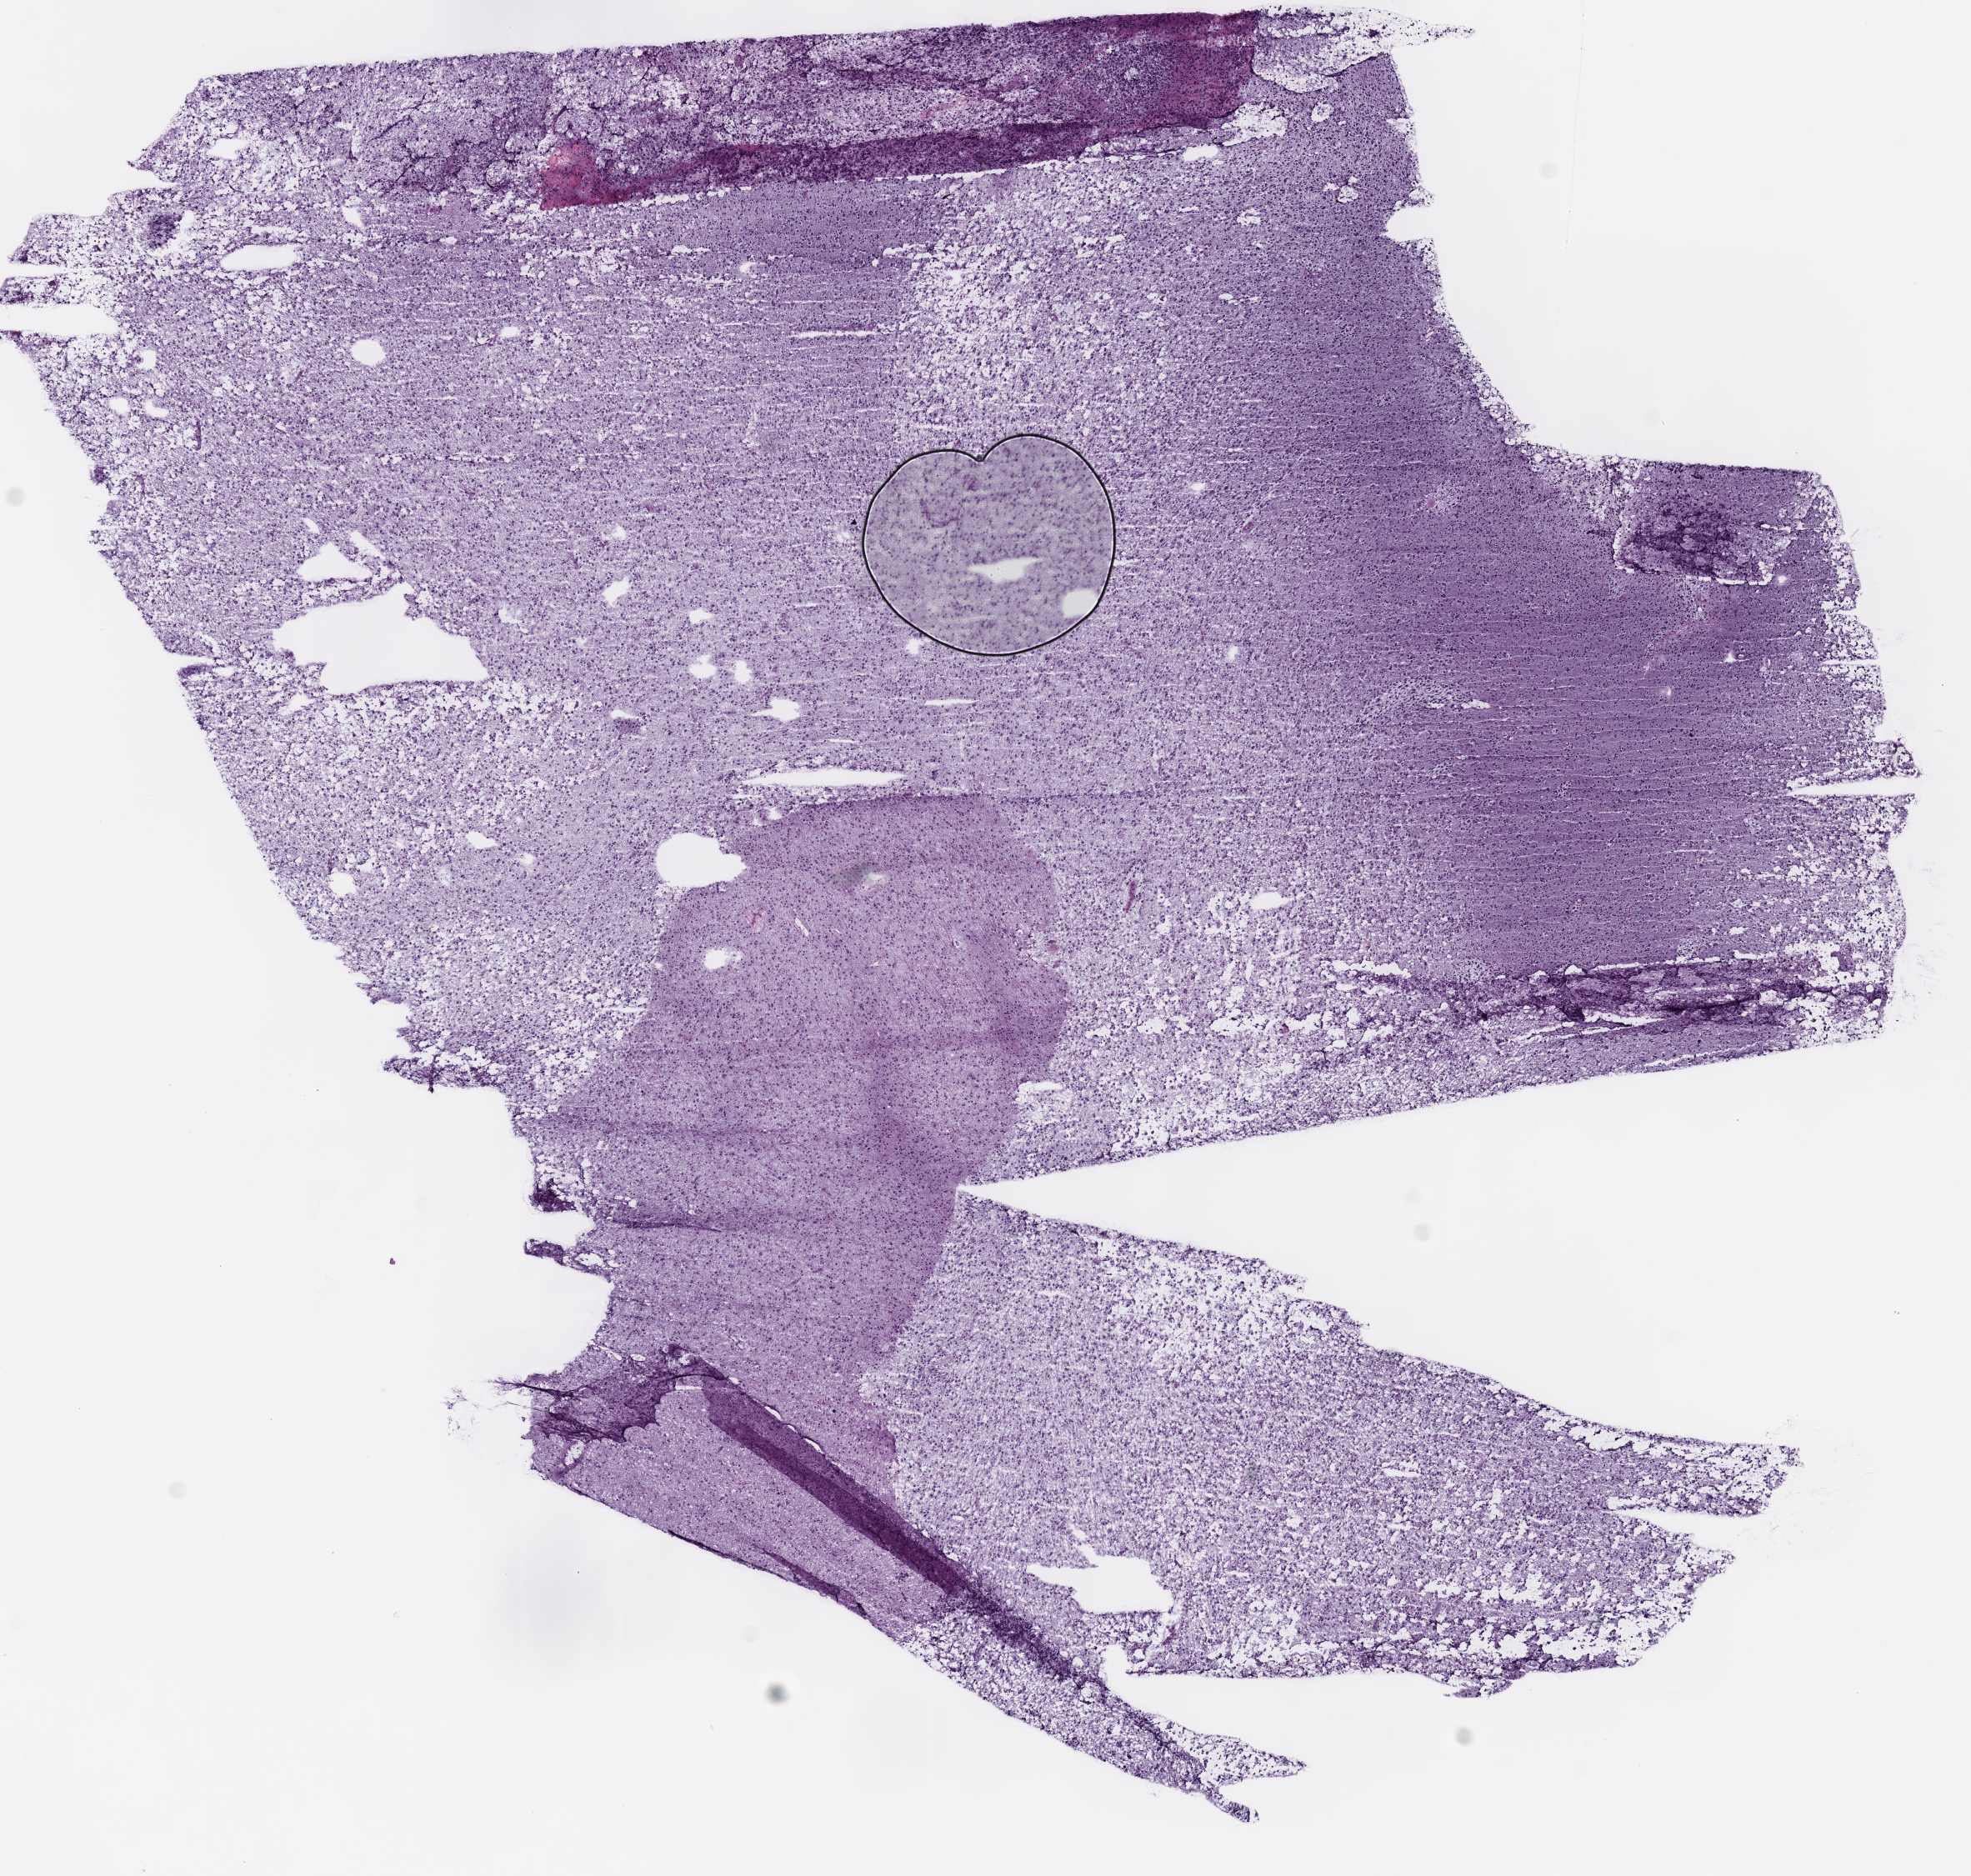
Digitized Hematoxylin and eosin (H&E) stained tissue section (whole slide) — a low-resolution overview of the entire scanned area, about 9.3 x 8.9 mm, frozen section, sample: primary tumour, brain. Patient: female, age at initial diagnosis 29 years. Histologic grade: G2 (moderately differentiated). Composition of this section per pathologist review: tumour cells 100%, tumour nuclei 85%, normal cells 0%, stromal cells 0%, necrosis 0%.
Laterality: left. Pathologic diagnosis: Mixed glioma (cerebrum).